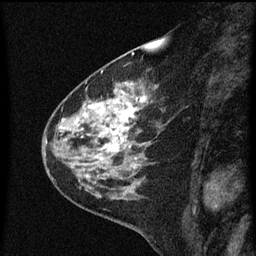
Breast MRI (dynamic contrast-enhanced), one sagittal slice; position 21 of 60 along the scan axis; dynamic contrast-enhanced series, image 2 of 3 at this slice position (ordered by acquisition); 1.5 T; TE 4.2 ms, TR 8 ms; 2 mm slice thickness; 256 × 256 image matrix, field of view 180 × 180 mm. Female patient, age 60 years.
Structures marked on this image (semi-automatic segmentation, software-assisted and operator-edited):
- analysis volume of interest (the breast-tissue region the enhancement analysis was run in; not a lesion): bounding box (x1, y1, x2, y2) in pixels: (48, 82, 159, 183)
- tumour enhancement mask (voxels above the 70 % enhancement threshold inside the analysis volume of interest): (63, 98, 145, 161)